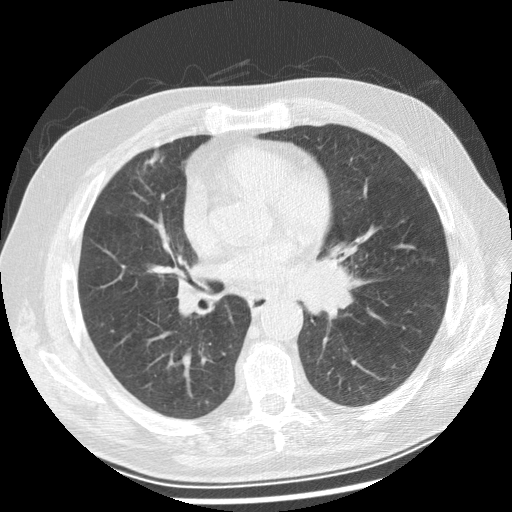
Low-dose screening chest CT, one axial slice. Position 129 of 250 along the scan axis. Reconstruction kernel STANDARD. 120 kVp. Lung window (W 1500 / L -600 HU). 2.5 mm slice thickness. 512 × 512 image matrix.
Structures marked on this image (manually delineated by an expert):
- lesion 1 (tumor, left main bronchus): bounding box [x1, y1, x2, y2] px = [296, 258, 361, 319]